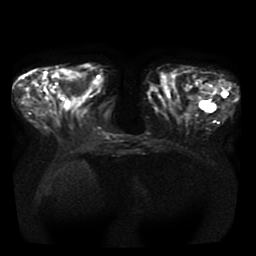
Breast MRI, one axial slice; position 12 of 41 along the scan axis; diffusion-weighted series; image 2 of 4 stored at this slice position (different b-values; order by instance number); 1.5 T; 5 mm slice thickness; 256 × 256 image matrix, field of view 350 × 350 mm. Female patient.
Annotated regions visible in this slice (expert manual segmentation):
- tumour on diffusion-weighted imaging: box from (x=34, y=73) to (x=46, y=82) px